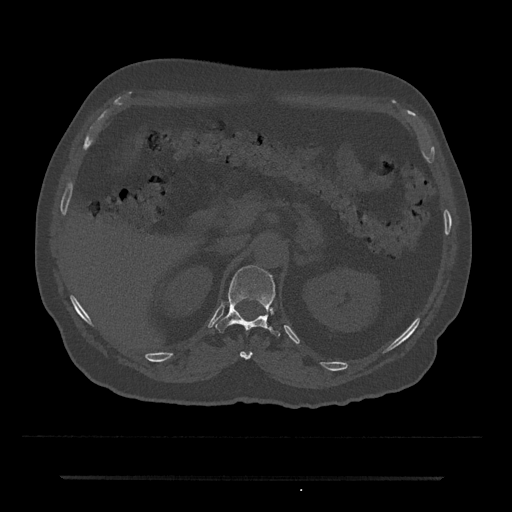
CT including the spine, one axial slice. Slice 131 of 797 in the series (ordered by position). 120 kVp. Bone window (W 1800 / L 400 HU). 0.5 mm slice thickness. 512 × 512 image matrix, field of view 437 × 437 mm. Patient: male, 69 years. Case-level facts recorded for this patient, not image findings: primary cancer: prostate.
Structures marked on this image (semi-automatically segmented with operator editing):
- T11 vertebra: bounding box (x1, y1, x2, y2) in pixels: (240, 351, 252, 360)
- T12 vertebra: (215, 265, 280, 336)